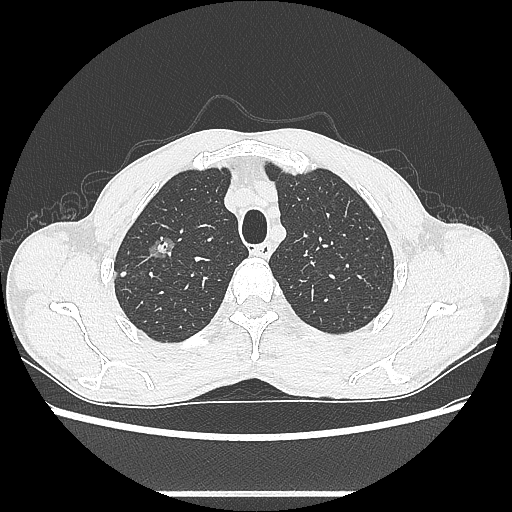
Chest CT, one axial slice; position 488 of 601 along the scan axis; reconstruction kernel LUNG; 100 kVp; lung window (W 1500 / L -600 HU); 0.62 mm slice thickness; 512 × 512 image matrix, field of view 357 × 357 mm. Patient: male, 54 years. From the clinical record (not read from this slice): clinical TNM (as recorded): T1a N0 M0.
Structures marked on this image (rectangle marked by the reading radiologist):
- lung tumour (recorded histology: adenocarcinoma): box from (x=142, y=230) to (x=178, y=266) px